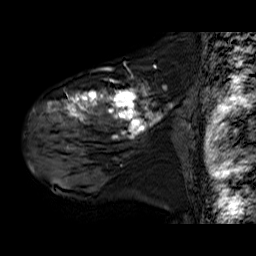
Breast MRI (dynamic contrast-enhanced), one sagittal slice. Dynamic contrast-enhanced series, time point 2 of 6 at this slice position (early post-contrast). 1.5 T. TE 6.3 ms, TR 32.9 ms. 4 mm slice thickness. 256 × 256 image matrix, field of view 200 × 200 mm. Female patient. From the clinical record (not read from this slice): setting: breast cancer imaged before/during neoadjuvant chemotherapy; receptor status: HER2-positive.
Structures marked on this image (semi-automatic segmentation, software-assisted and operator-edited):
- analysis volume of interest (the breast-tissue region the enhancement analysis was run in; not a lesion): bounding box <30,78,182,180> (left, top, right, bottom; pixels)
- tumour enhancement mask (voxels above the 100 % enhancement threshold inside the analysis volume of interest): <30,88,163,172>